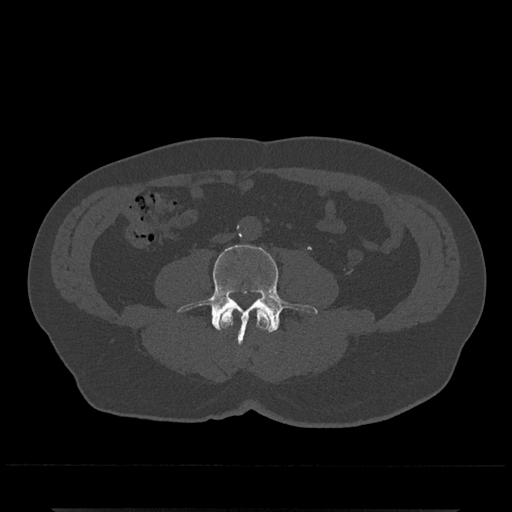
CT including the spine, one axial slice. Reconstruction kernel Br40s/3. 120 kVp. Bone window (W 1800 / L 400 HU). 0.5 mm slice thickness. 512 × 512 image matrix, field of view 393 × 393 mm. Male patient, age 67 years. From the clinical record (not read from this slice): primary cancer: prostate.
Structures marked on this image (semi-automatically segmented with operator editing):
- L3 vertebra: bounding box <219,307,271,332> (left, top, right, bottom; pixels)
- L4 vertebra: <177,244,318,344>